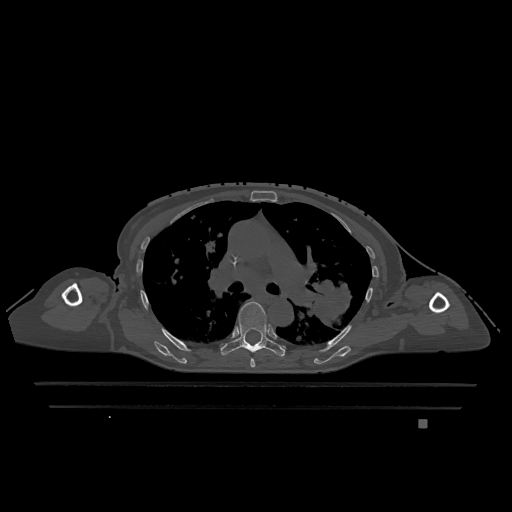
CT including the spine, one axial slice; slice 799 of 1317 in the series (ordered by position); bone window (W 1800 / L 400 HU); 0.5 mm slice thickness; 512 × 512 image matrix. Patient: female, 74 years. Case-level facts recorded for this patient, not image findings: primary cancer: lung.
Outlined on this slice (semi-automatic segmentation, software-assisted and operator-edited):
- T5 vertebra: box from (x=250, y=358) to (x=255, y=368) px
- T6 vertebra: (x=220, y=301)–(x=286, y=357)